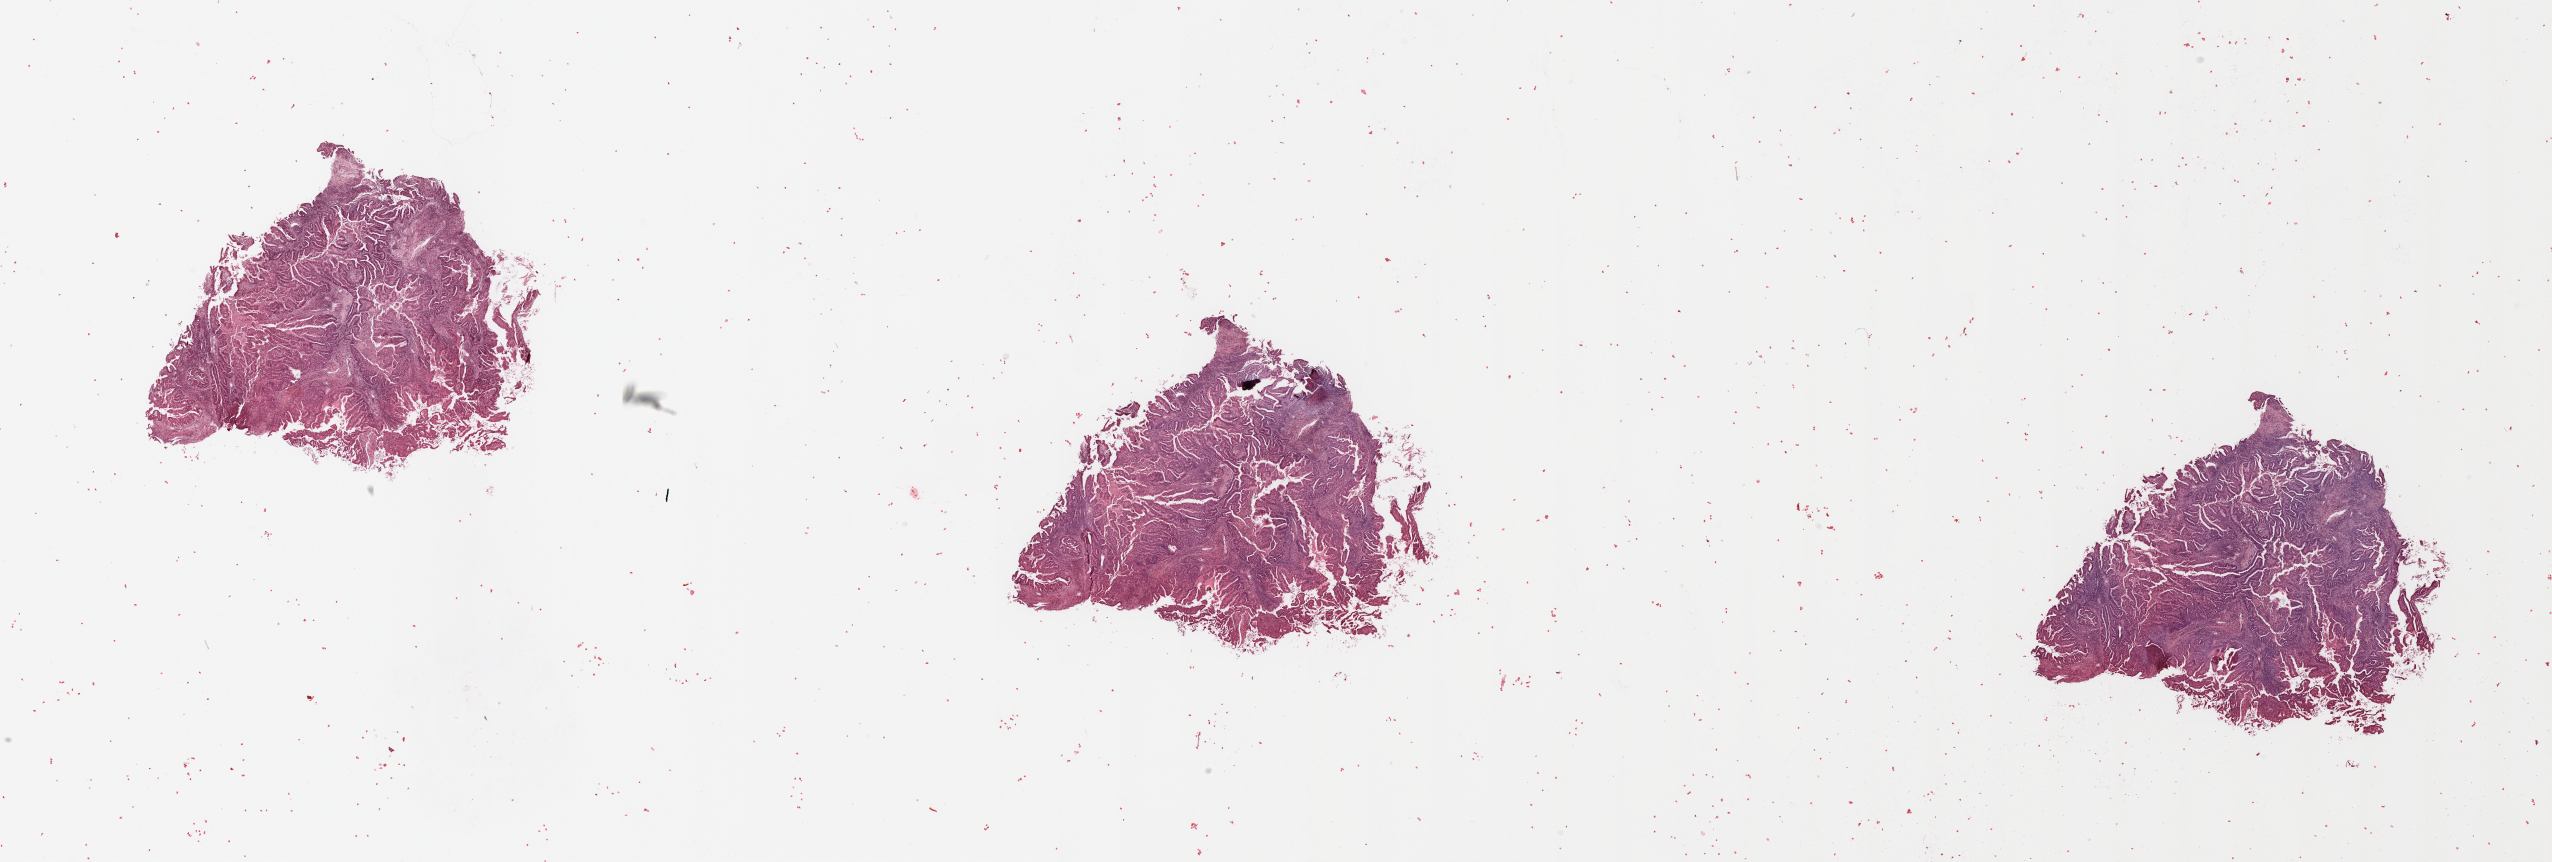
Digitized H&E-stained tissue section (whole slide), a low-resolution overview of the entire scanned area, about 40.4 x 13.6 mm (from a 20x scan). Tumour tissue sample, sampled site: uterus. Female, 59 y/o. Composition of this section per pathologist review: tumour nuclei 80%, necrosis 5%.
Diagnosis: Endometrioid adenocarcinoma, NOS.